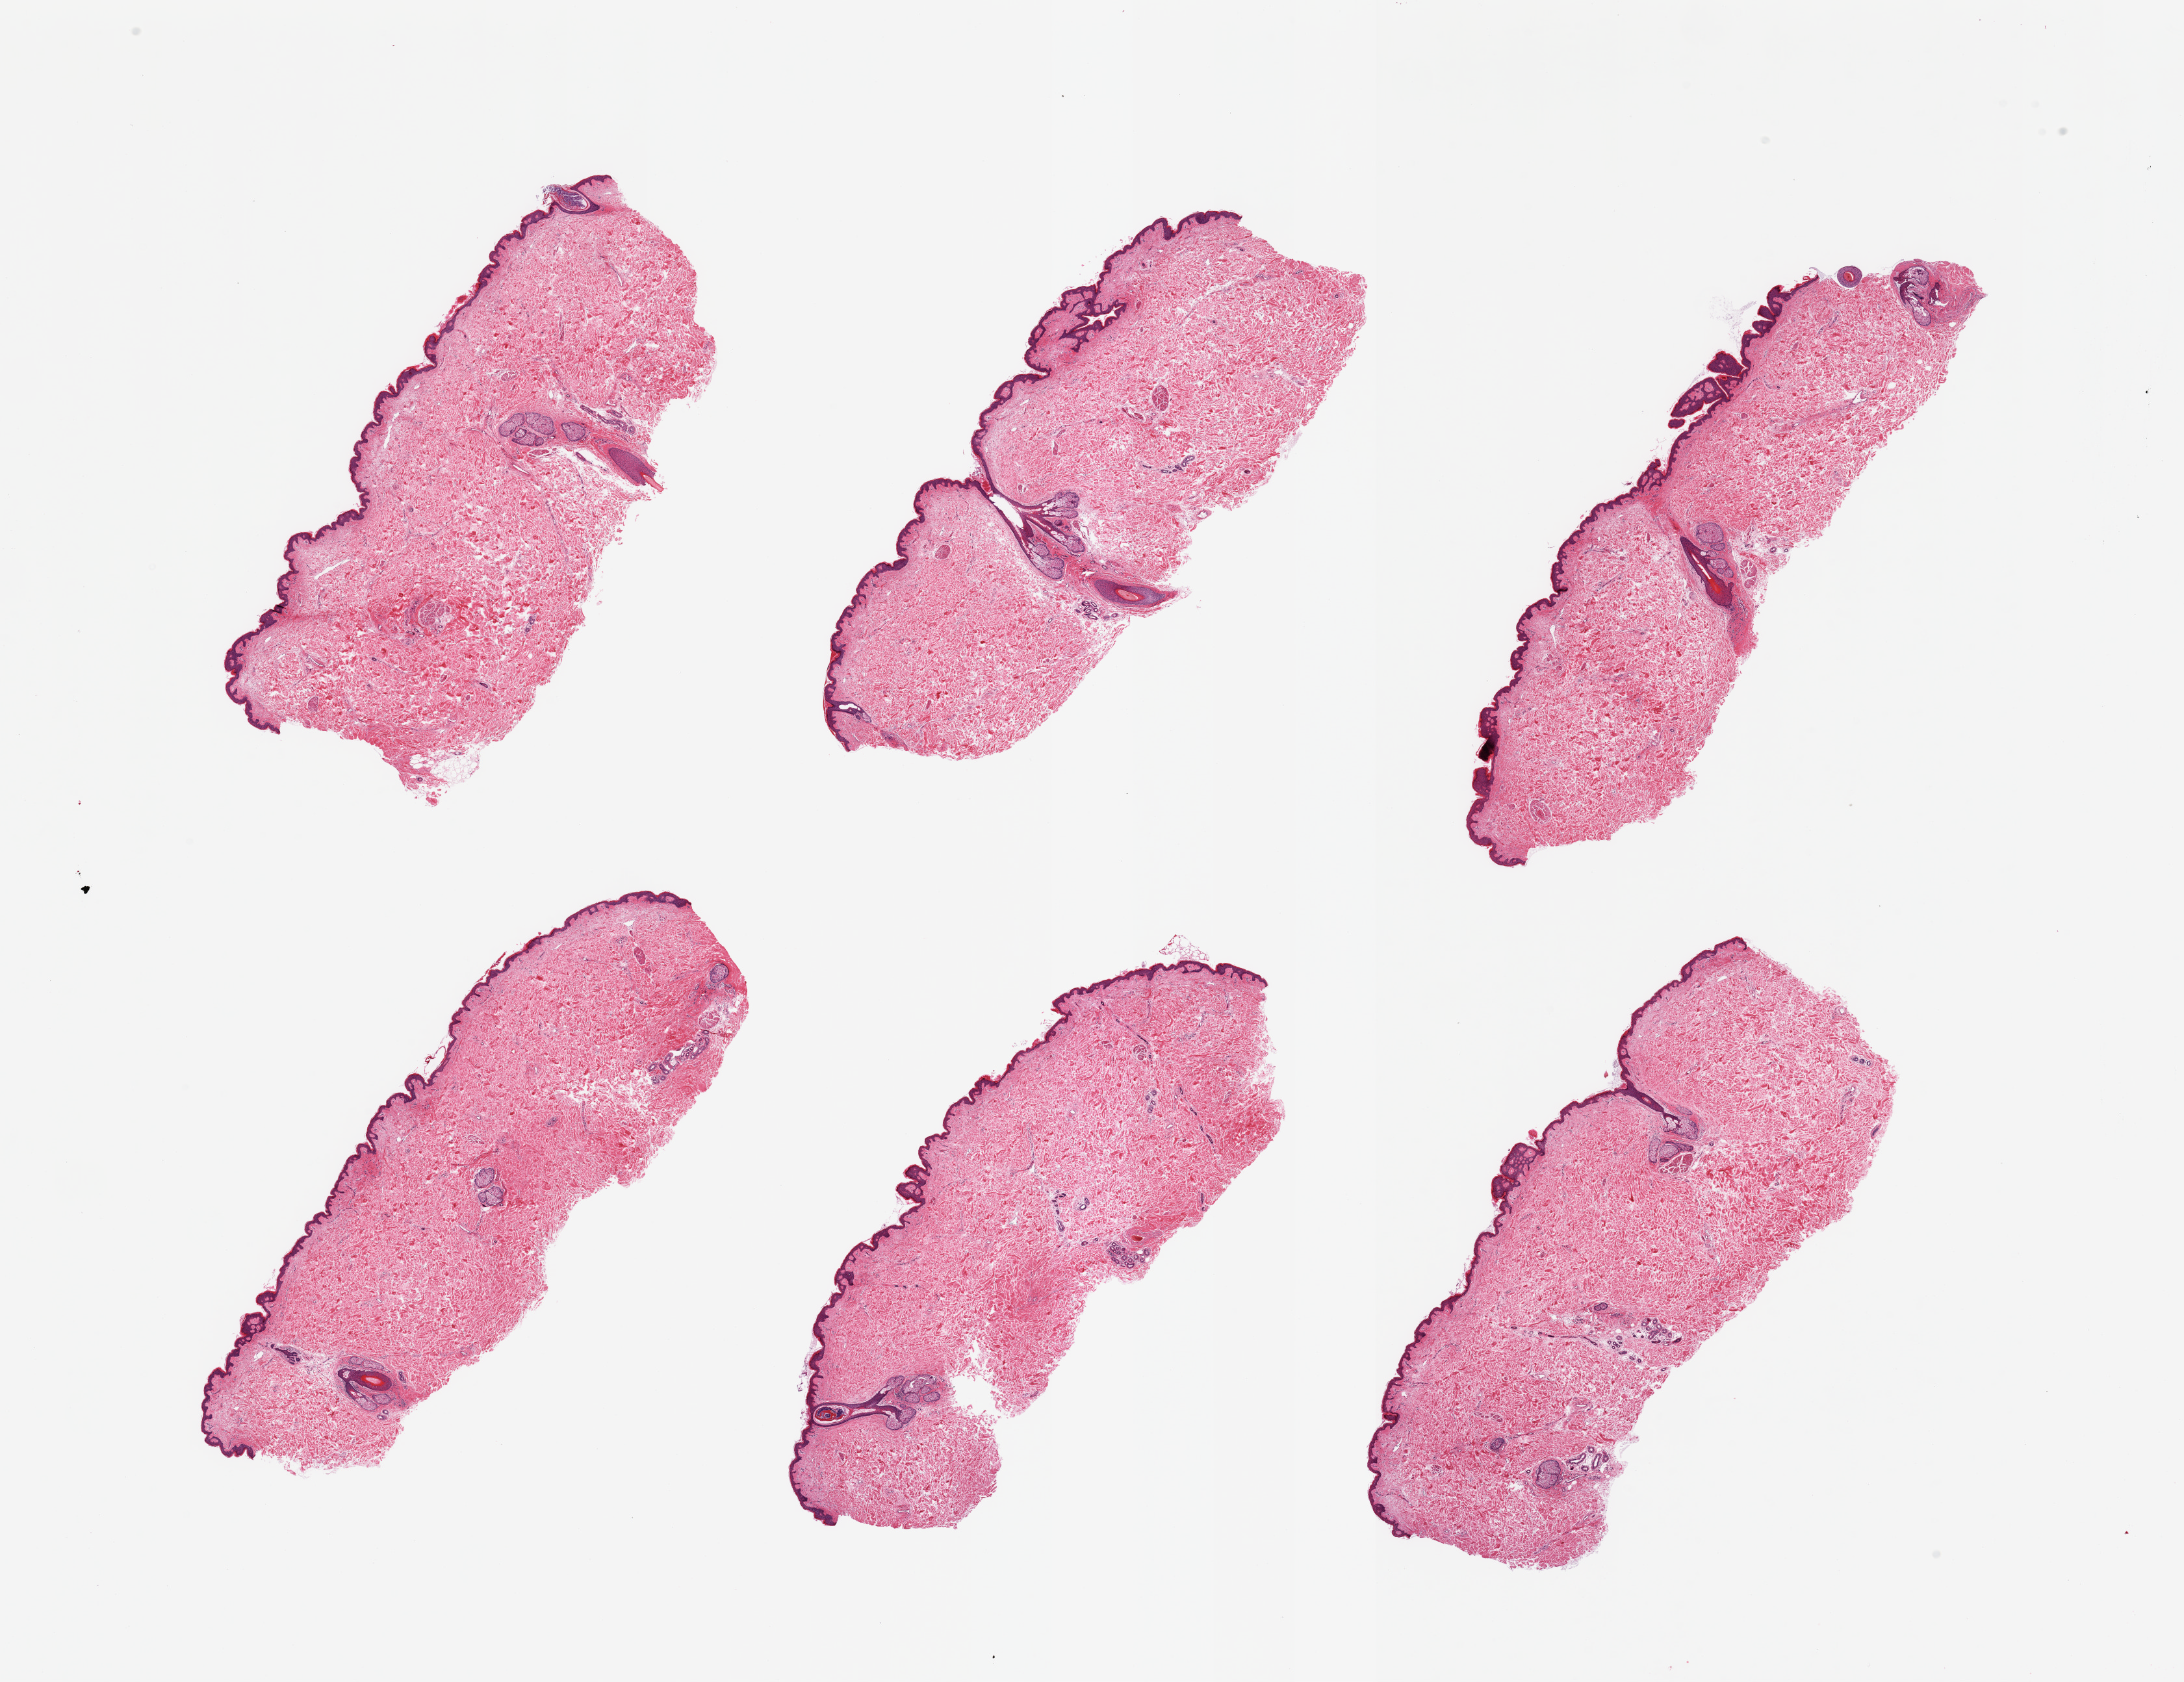
H&E whole-slide image — a low-resolution overview of the entire scanned area, about 26.6 x 20.5 mm (slide scanned at 20x). PAXgene-fixed paraffin-embedded (PFPE) section. Target tissue: skin of suprapubic region. Tissue donor sample.
Review note (as recorded): 6 pieces; well dissected; no dermal fat; single large hair complex in several pieces.